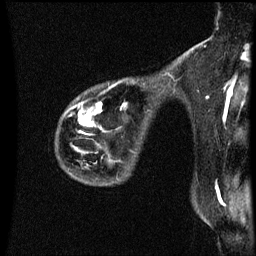
Breast MRI (dynamic contrast-enhanced), one sagittal slice; position 46 of 60 along the scan axis; dynamic contrast-enhanced series, image 2 of 3 at this slice position (ordered by acquisition); 1.5 T; TE 4.2 ms, TR 8.9 ms; 256 × 256 image matrix, field of view 200 × 200 mm. Female patient, age 44 years. From the clinical record (not read from this slice): setting: breast cancer imaged before/during neoadjuvant chemotherapy; receptor status: HR-positive, HER2-negative.
Structures marked on this image (semi-automatically segmented with operator editing):
- analysis volume of interest (the breast-tissue region the enhancement analysis was run in; not a lesion): box from (x=63, y=82) to (x=125, y=175) px
- tumour enhancement mask (voxels above the 70 % enhancement threshold inside the analysis volume of interest): (x=89, y=104)–(x=102, y=125)